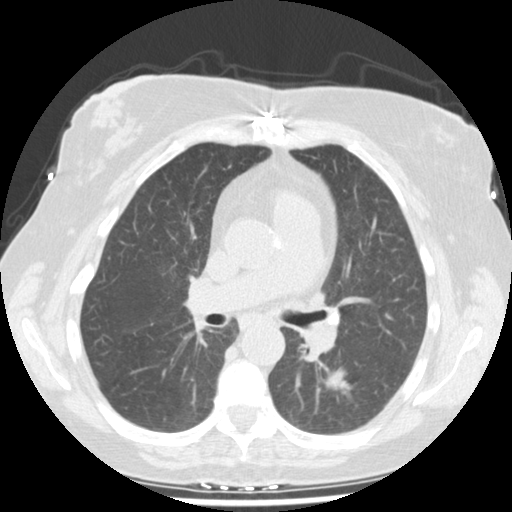
Low-dose screening chest CT, axial slice. Second screening round (one year after baseline). Lung window (W 1500 / L -600 HU). 2.5 mm slice thickness. Standard (soft-tissue) reconstruction kernel (STANDARD). 120 kVp. Slice 62 of 159 in the series. Female participant, aged 61 years at enrolment. Current smoker at enrolment.
Expert reader's lesion annotation, box from (x=312, y=355) to (x=369, y=407) px. The screening reader recorded 2 non-calcified nodules or masses ≥4 mm on this exam (left lower lobe, right upper lobe); which of them this box marks is not recorded. Lung cancer was diagnosed 69 days after this screen: squamous cell carcinoma, NOS, left lower lobe, moderately differentiated (G2), stage IA (AJCC 6th edition), 12 mm at pathology.